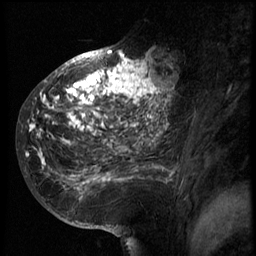
Breast MRI (dynamic contrast-enhanced), one sagittal slice. Slice 33 of 66 in the series (ordered by position). 3 images stored at this slice position (order not interpretable as contrast timing). 1.5 T. TE 4.2 ms, TR 8.9 ms. 256 × 256 image matrix, field of view 200 × 200 mm. Female patient, age 39 years. From the clinical record (not read from this slice): setting: breast cancer imaged before/during neoadjuvant chemotherapy; receptor status: HER2-positive.
Annotated regions visible in this slice (semi-automatically segmented with operator editing):
- analysis volume of interest (the breast-tissue region the enhancement analysis was run in; not a lesion): bounding box [x1, y1, x2, y2] px = [29, 44, 166, 196]
- tumour enhancement mask (voxels above the 140 % enhancement threshold inside the analysis volume of interest): [29, 50, 166, 184]